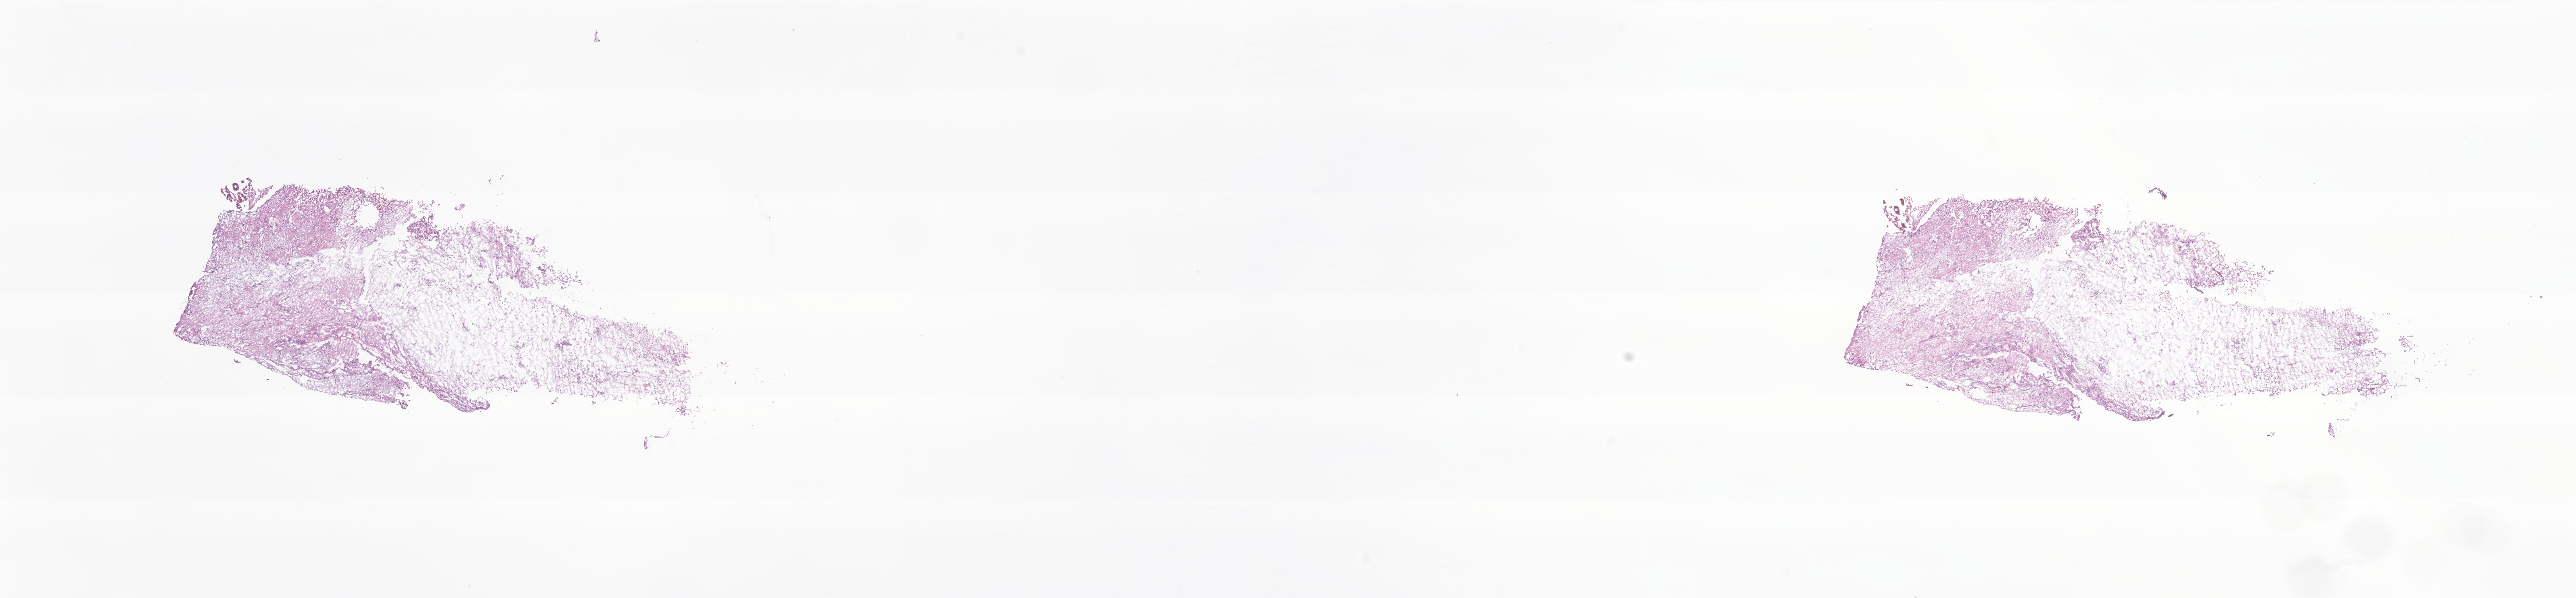
Digitized H&E-stained section of tumor tissue from the brain, shown as a low-resolution overview of the whole scanned area (about 26.9 x 6.3 mm); frozen section. Male patient, age 101 months.
Diagnosis: Neoplasm, malignant.